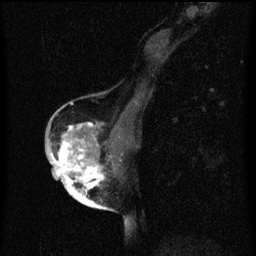
Breast MRI (dynamic contrast-enhanced), one sagittal slice; slice 30 of 60 in the series (ordered by position); dynamic contrast-enhanced series, image 2 of 3 at this slice position (ordered by acquisition); 1.5 T; TE 4.2 ms, TR 8 ms; 2 mm slice thickness; 256 × 256 image matrix, field of view 180 × 180 mm. Patient: female, 56 years.
Outlined on this slice (semi-automatic segmentation, software-assisted and operator-edited):
- analysis volume of interest (the breast-tissue region the enhancement analysis was run in; not a lesion): bounding box <54,124,120,199> (left, top, right, bottom; pixels)
- tumour enhancement mask (voxels above the 70 % enhancement threshold inside the analysis volume of interest): <54,124,105,199>